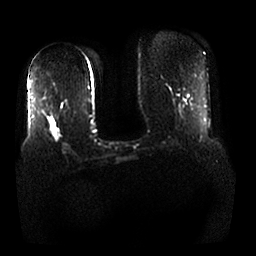
Breast MRI, one axial slice; slice 12 of 25 in the series (ordered by position); diffusion-weighted series; image 2 of 4 stored at this slice position (different b-values; order by instance number); 1.5 T; 256 × 256 image matrix. Female patient.
Annotated regions visible in this slice (outlined manually by an expert reader):
- tumour on diffusion-weighted imaging: bounding box <54,131,60,142> (left, top, right, bottom; pixels)